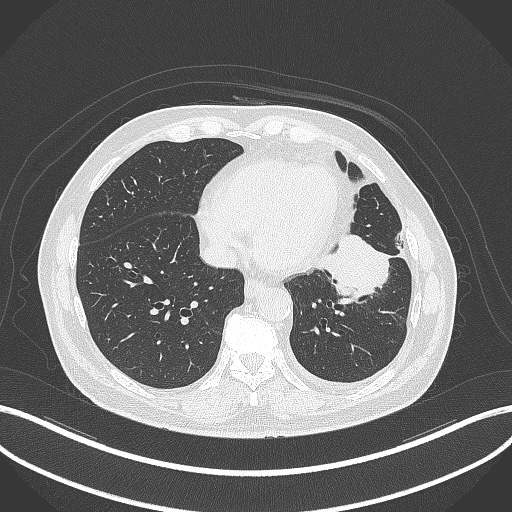
Chest CT, one axial slice; slice 114 of 230 in the series (ordered by position); 120 kVp; lung window (W 1500 / L -600 HU); 1 mm slice thickness; 512 × 512 image matrix. Patient: male, 68 years. Case-level facts recorded for this patient, not image findings: clinical TNM (as recorded): T2b N0 M0.
Outlined on this slice (bounding box drawn by a radiologist):
- lung tumour (recorded histology: squamous cell carcinoma): box from (x=315, y=231) to (x=394, y=307) px